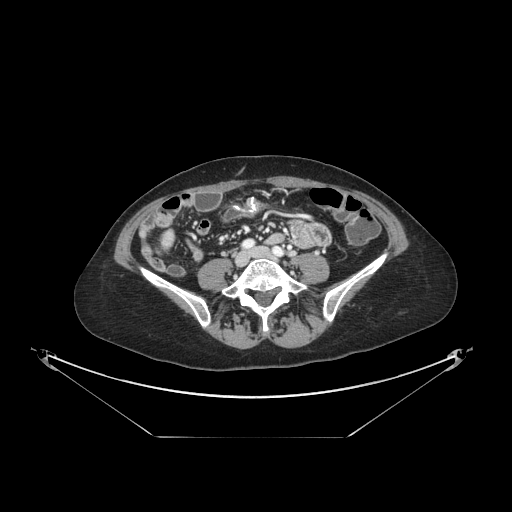
Contrast-enhanced abdominal CT, one axial slice. Slice 14 of 148 in the series (ordered by position). Reconstruction kernel STANDARD. Intravenous contrast given. Soft-tissue window (W 400 / L 40 HU). 2.5 mm slice thickness. 512 × 512 image matrix, field of view 500 × 500 mm. Female patient, age 73 years. Case-level facts recorded for this patient, not image findings: diagnosis: colorectal cancer liver metastases, imaged before liver resection; multiple liver metastases: no; largest metastasis: 1 cm.
Structures marked on this image (manually delineated by an expert):
- liver: bounding box <166,236,170,244> (left, top, right, bottom; pixels)